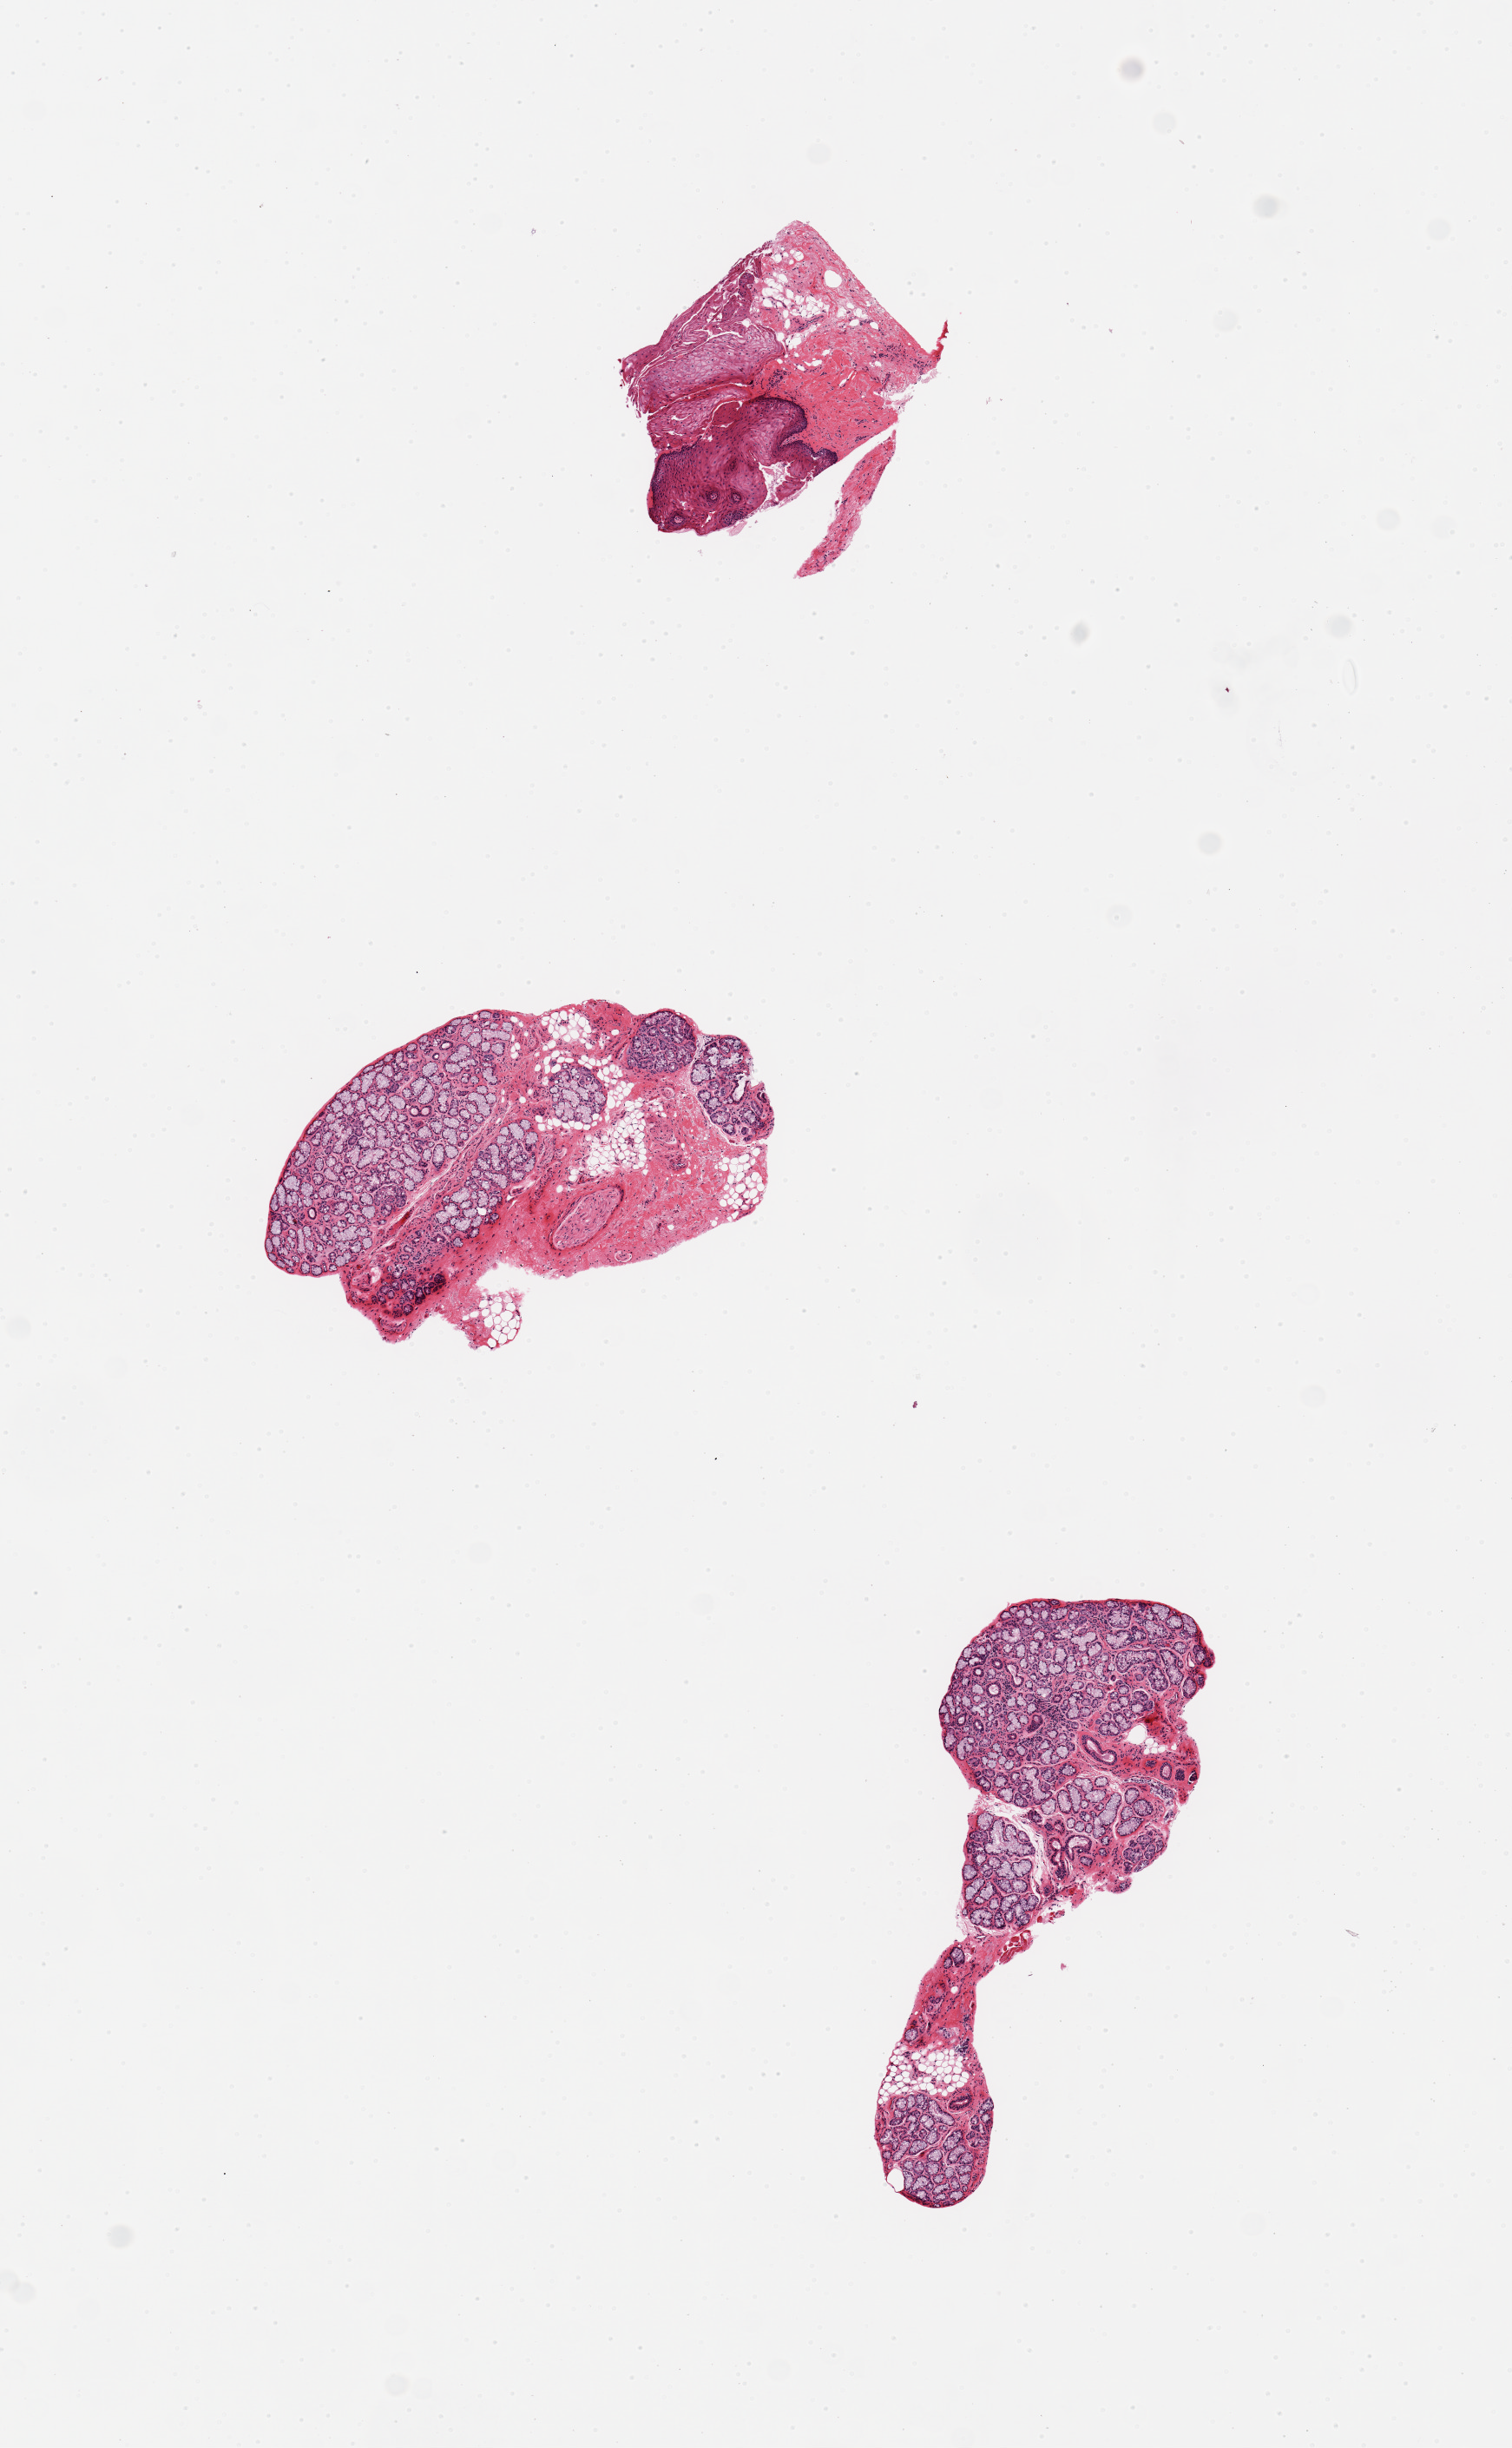
Digitized H&E-stained section, brightfield — a low-resolution overview of the entire scanned area, about 6.9 x 11.2 mm (from a 20x scan). PAXgene-fixed, paraffin-embedded tissue. Target tissue: minor salivary gland. Tissue donor sample. Male donor.
• reviewer comment on this tissue sample: 3 pieces, excellent specimen, does include smaller piece of lip, but good composite representation of salivary glands